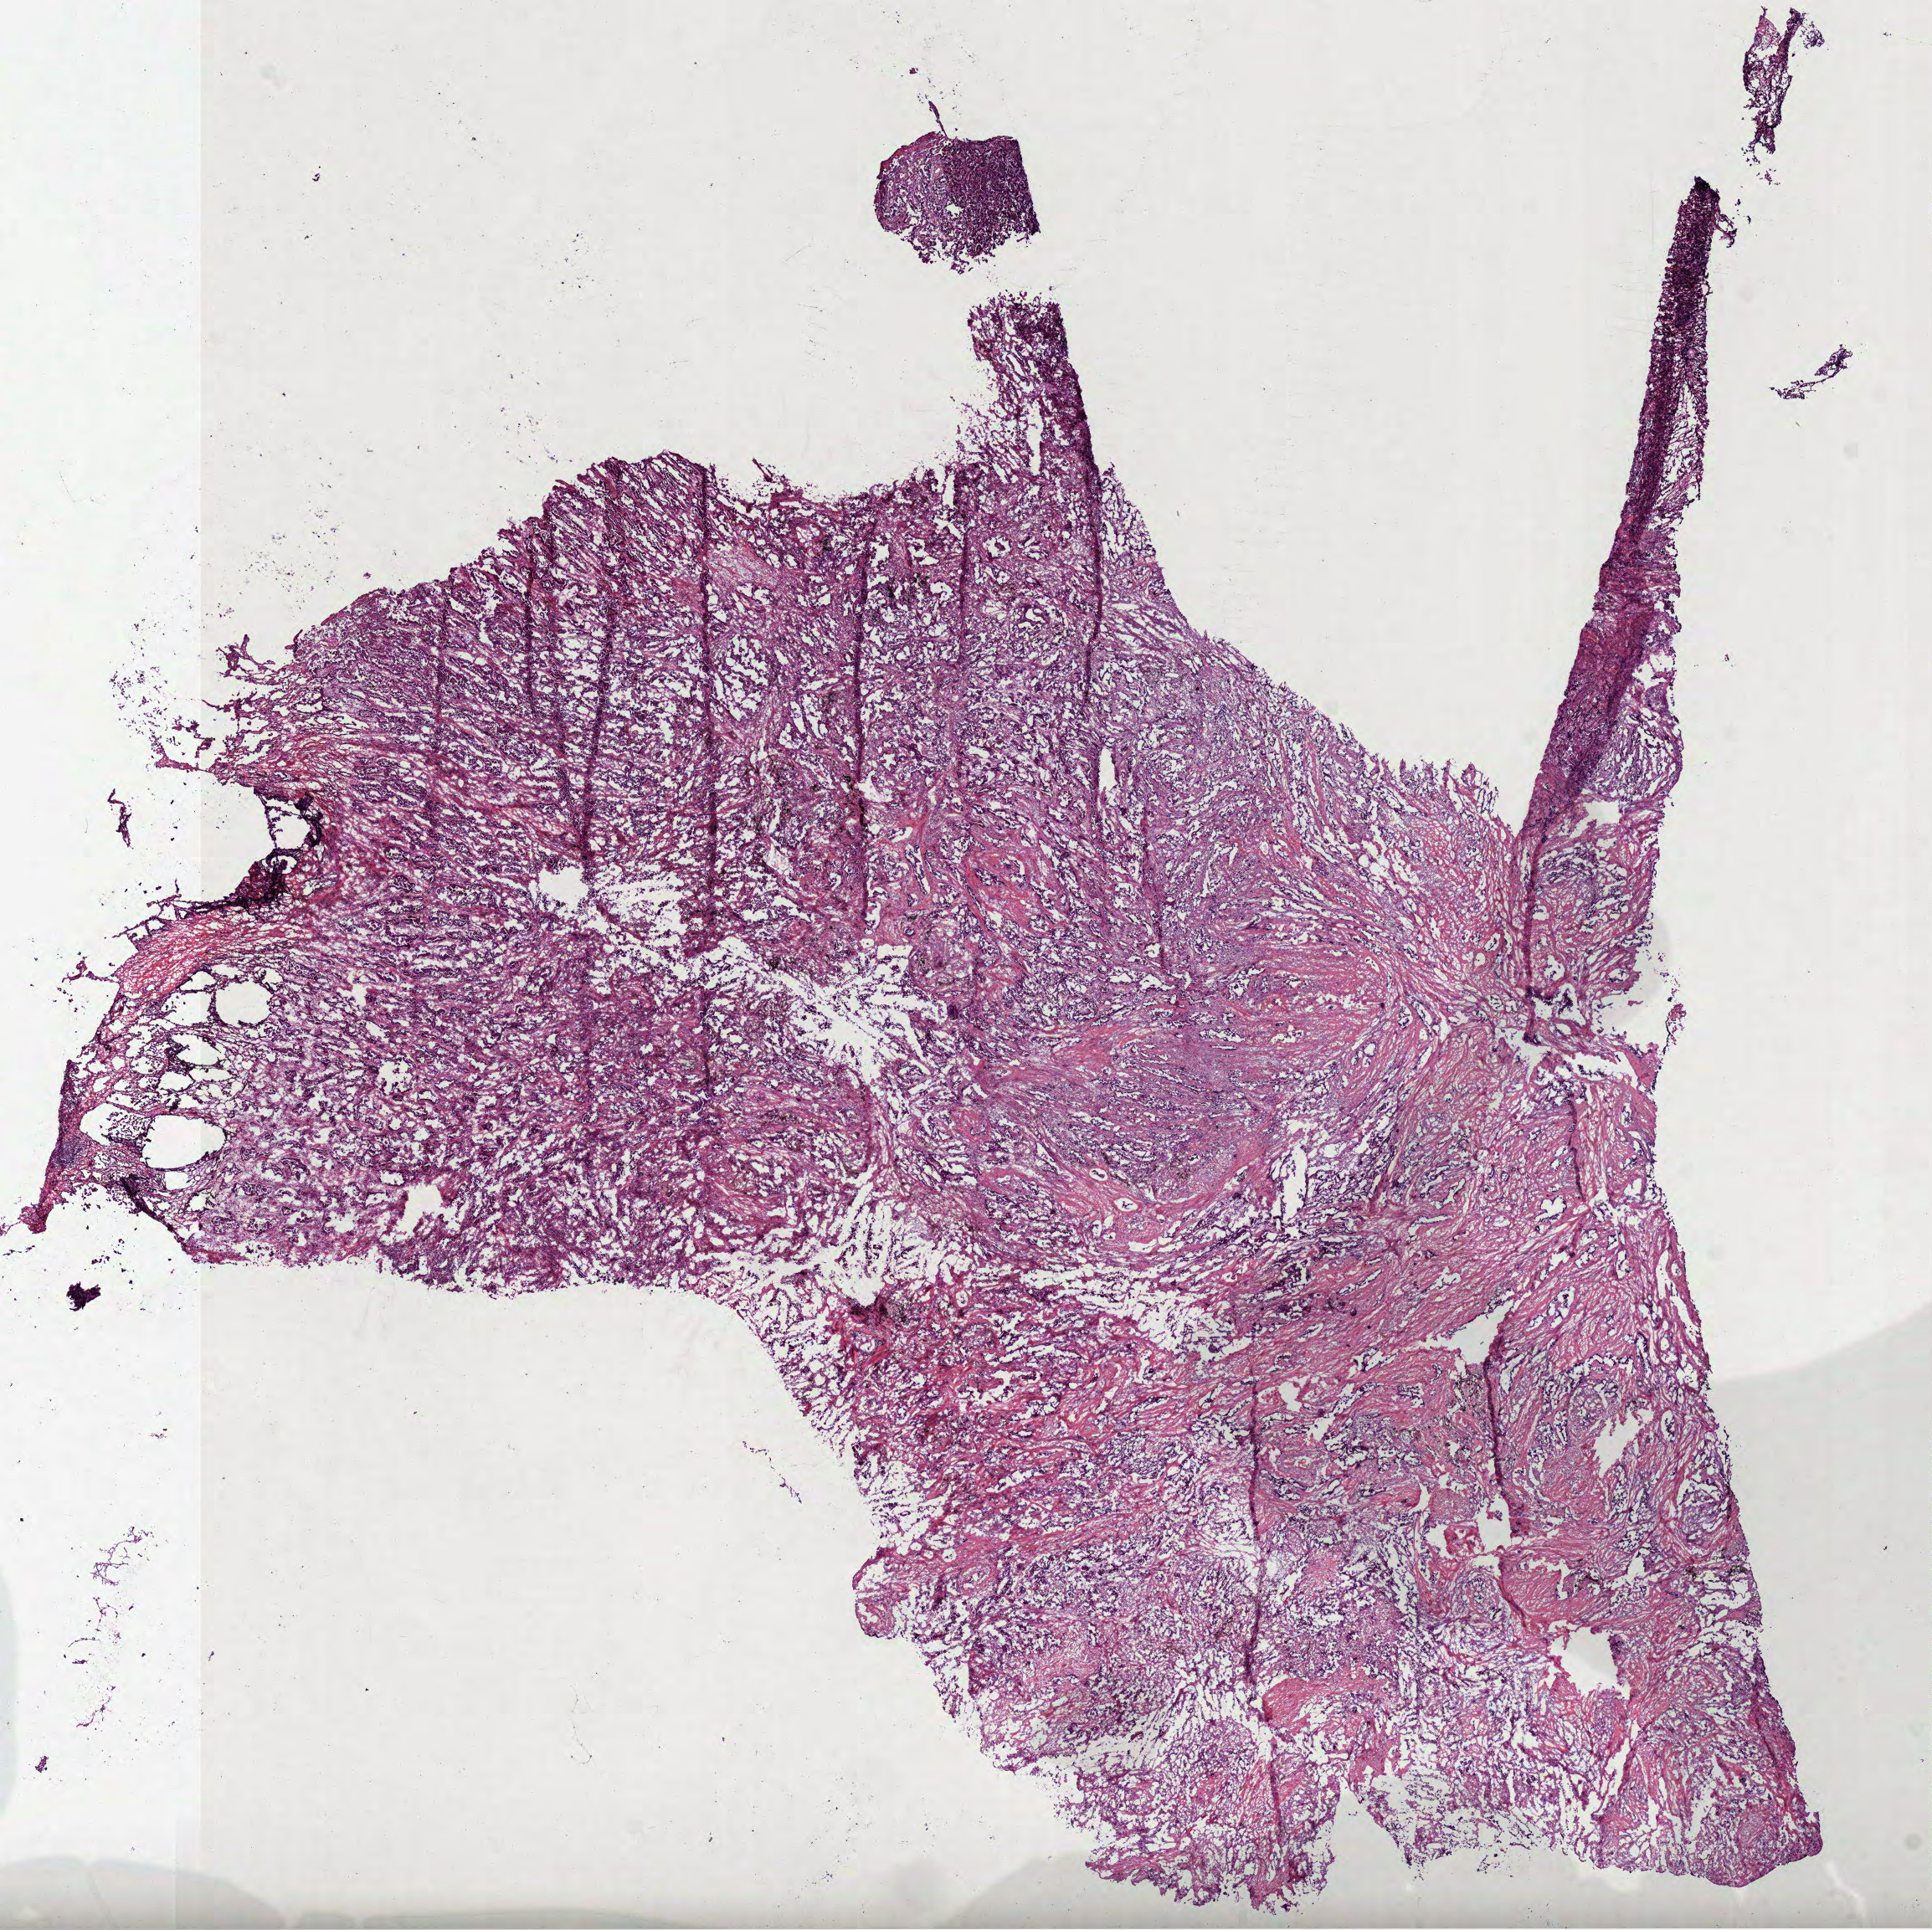
Whole-slide histology image, H&E-stained — low-resolution overview of the scanned area, about 18.6 x 18.6 mm (from a 40x scan); frozen section from the bottom of the tissue portion; lung, primary tumour sample. Patient: male, age at initial diagnosis 46 years. Pathologist review of this section (percent, as recorded): tumour cells 77%, tumour nuclei 80%, normal cells 0%, stromal cells 15%, necrosis 8%.
* pathologic diagnosis: Adenocarcinoma, NOS (upper lobe, lung)
* AJCC pathologic stage: IIA (7th edition)